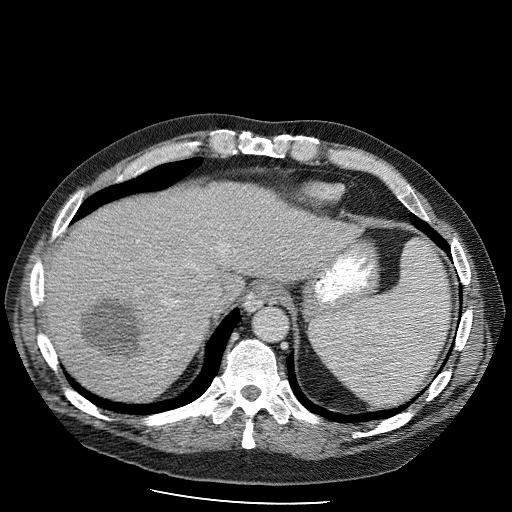
Contrast-enhanced abdominal CT (liver protocol), one axial slice; slice 83 of 98 in the series (ordered by position); reconstruction kernel STANDARD; soft-tissue window (W 400 / L 40 HU); 2.5 mm slice thickness; 512 × 512 image matrix, field of view 400 × 400 mm. From the clinical record (not read from this slice): diagnosis: hepatocellular carcinoma (patient treated with transarterial chemoembolisation; whether this scan precedes or follows treatment is not stated here); TNM stage (as recorded): Stage-II; Child-Pugh class: B; tumour differentiation: moderately differentiated; tumour nodularity: uninodular.
Structures marked on this image (semi-automatic segmentation, software-assisted and operator-edited):
- liver parenchyma outside the tumour (the mass and vessels are separate outlines, so this box may not span the whole liver): bounding box <42,184,352,392> (left, top, right, bottom; pixels)
- mass: <76,292,152,363>